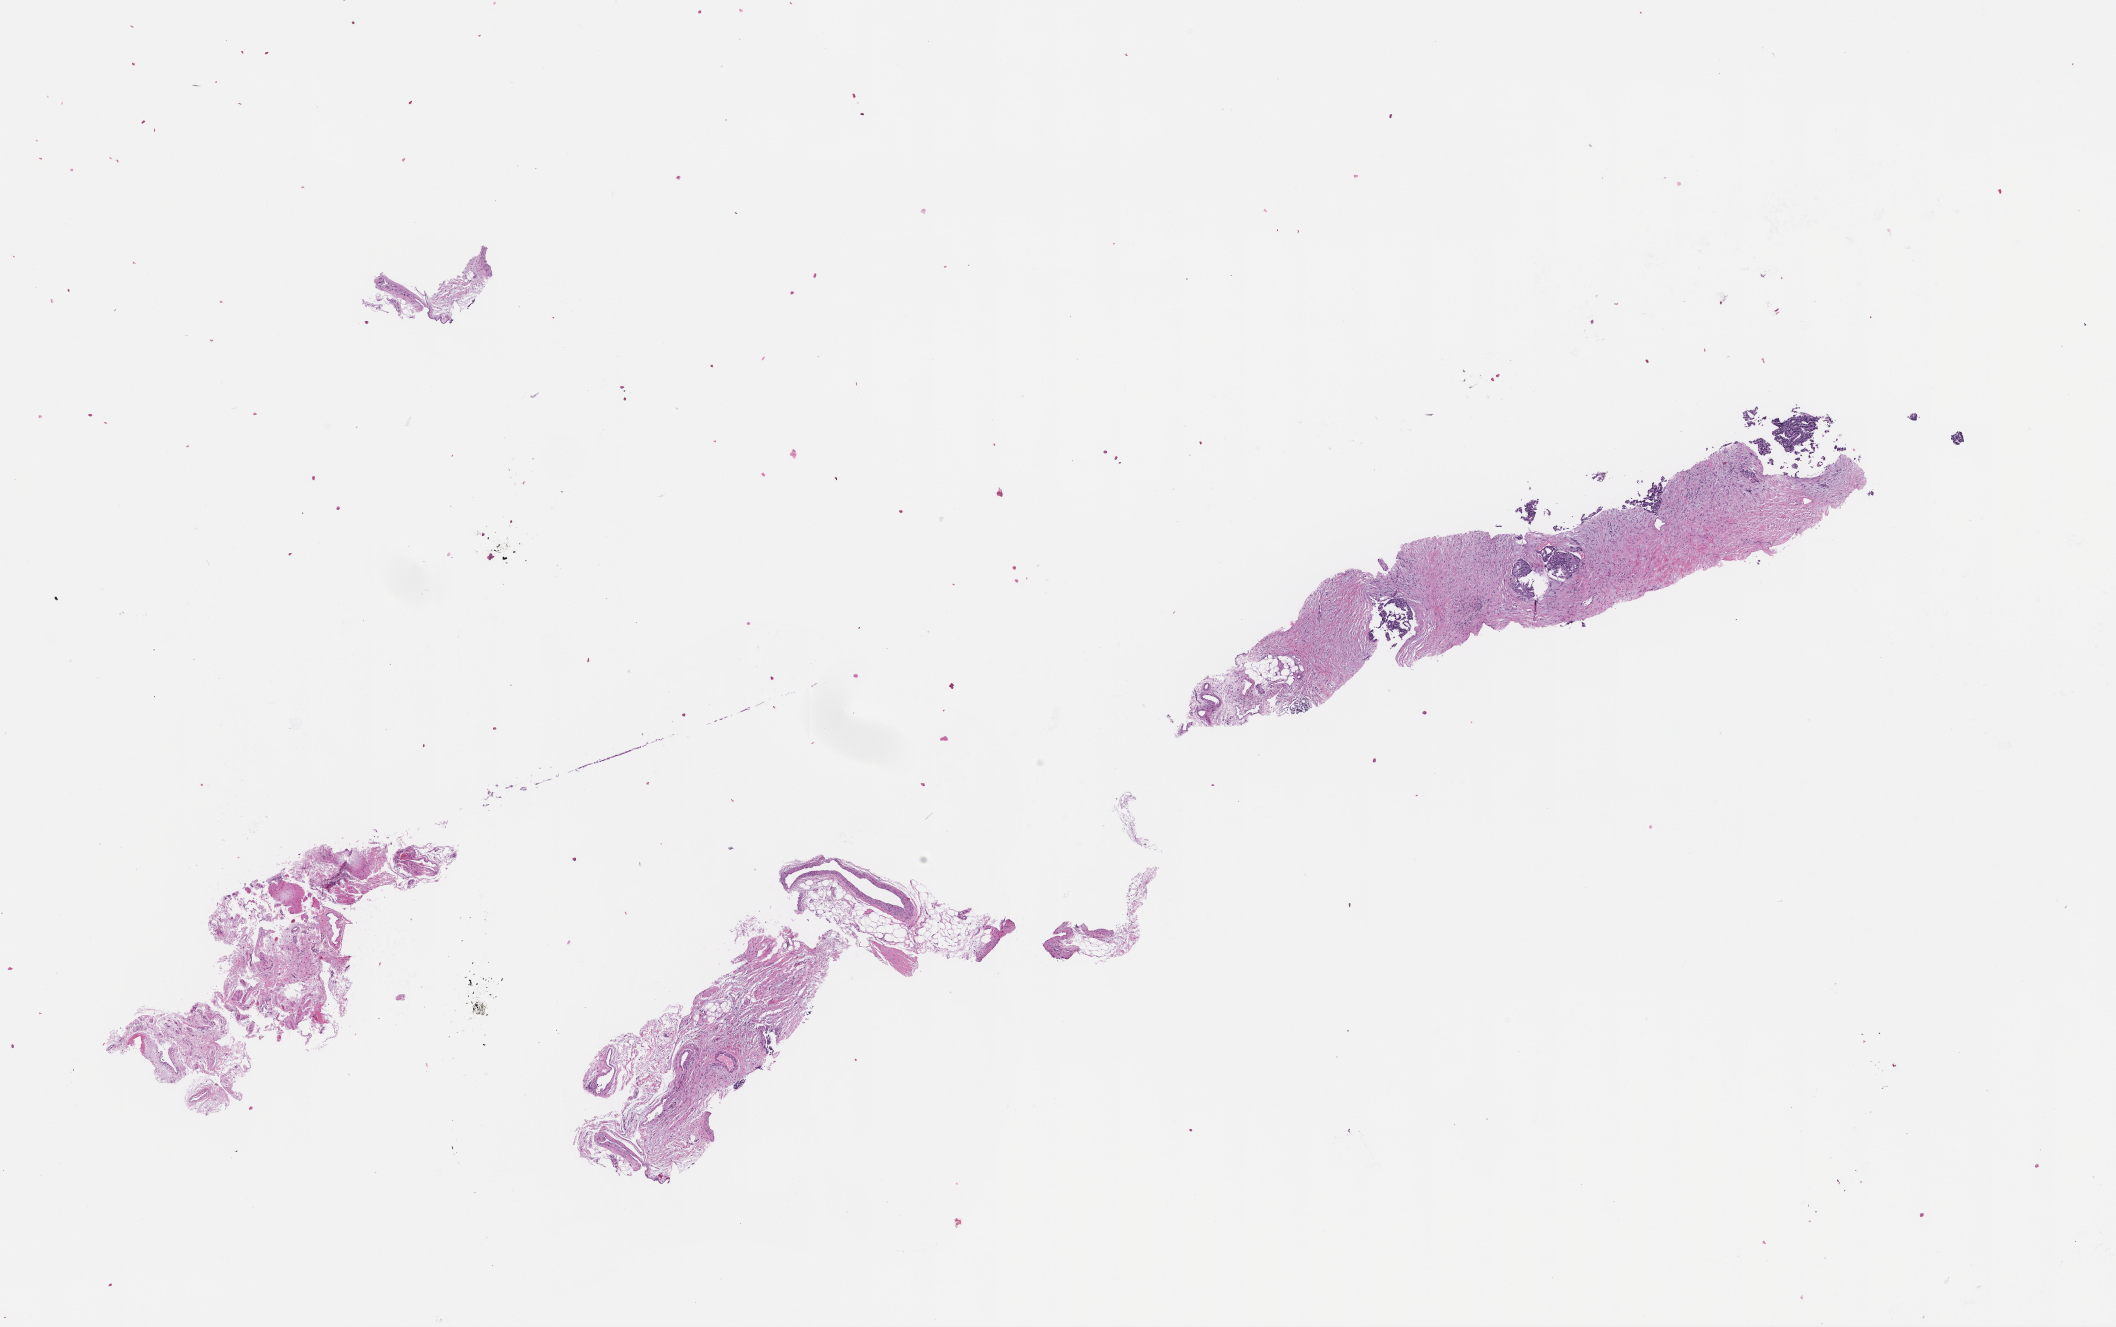
Whole-slide image, haematoxylin and eosin stain — low-resolution overview of the scanned area, about 17.1 x 10.7 mm; formalin-fixed paraffin-embedded section; site: prostate. Male patient.
This section: primary tumor. Diagnosis: Prostate Carcinoma.